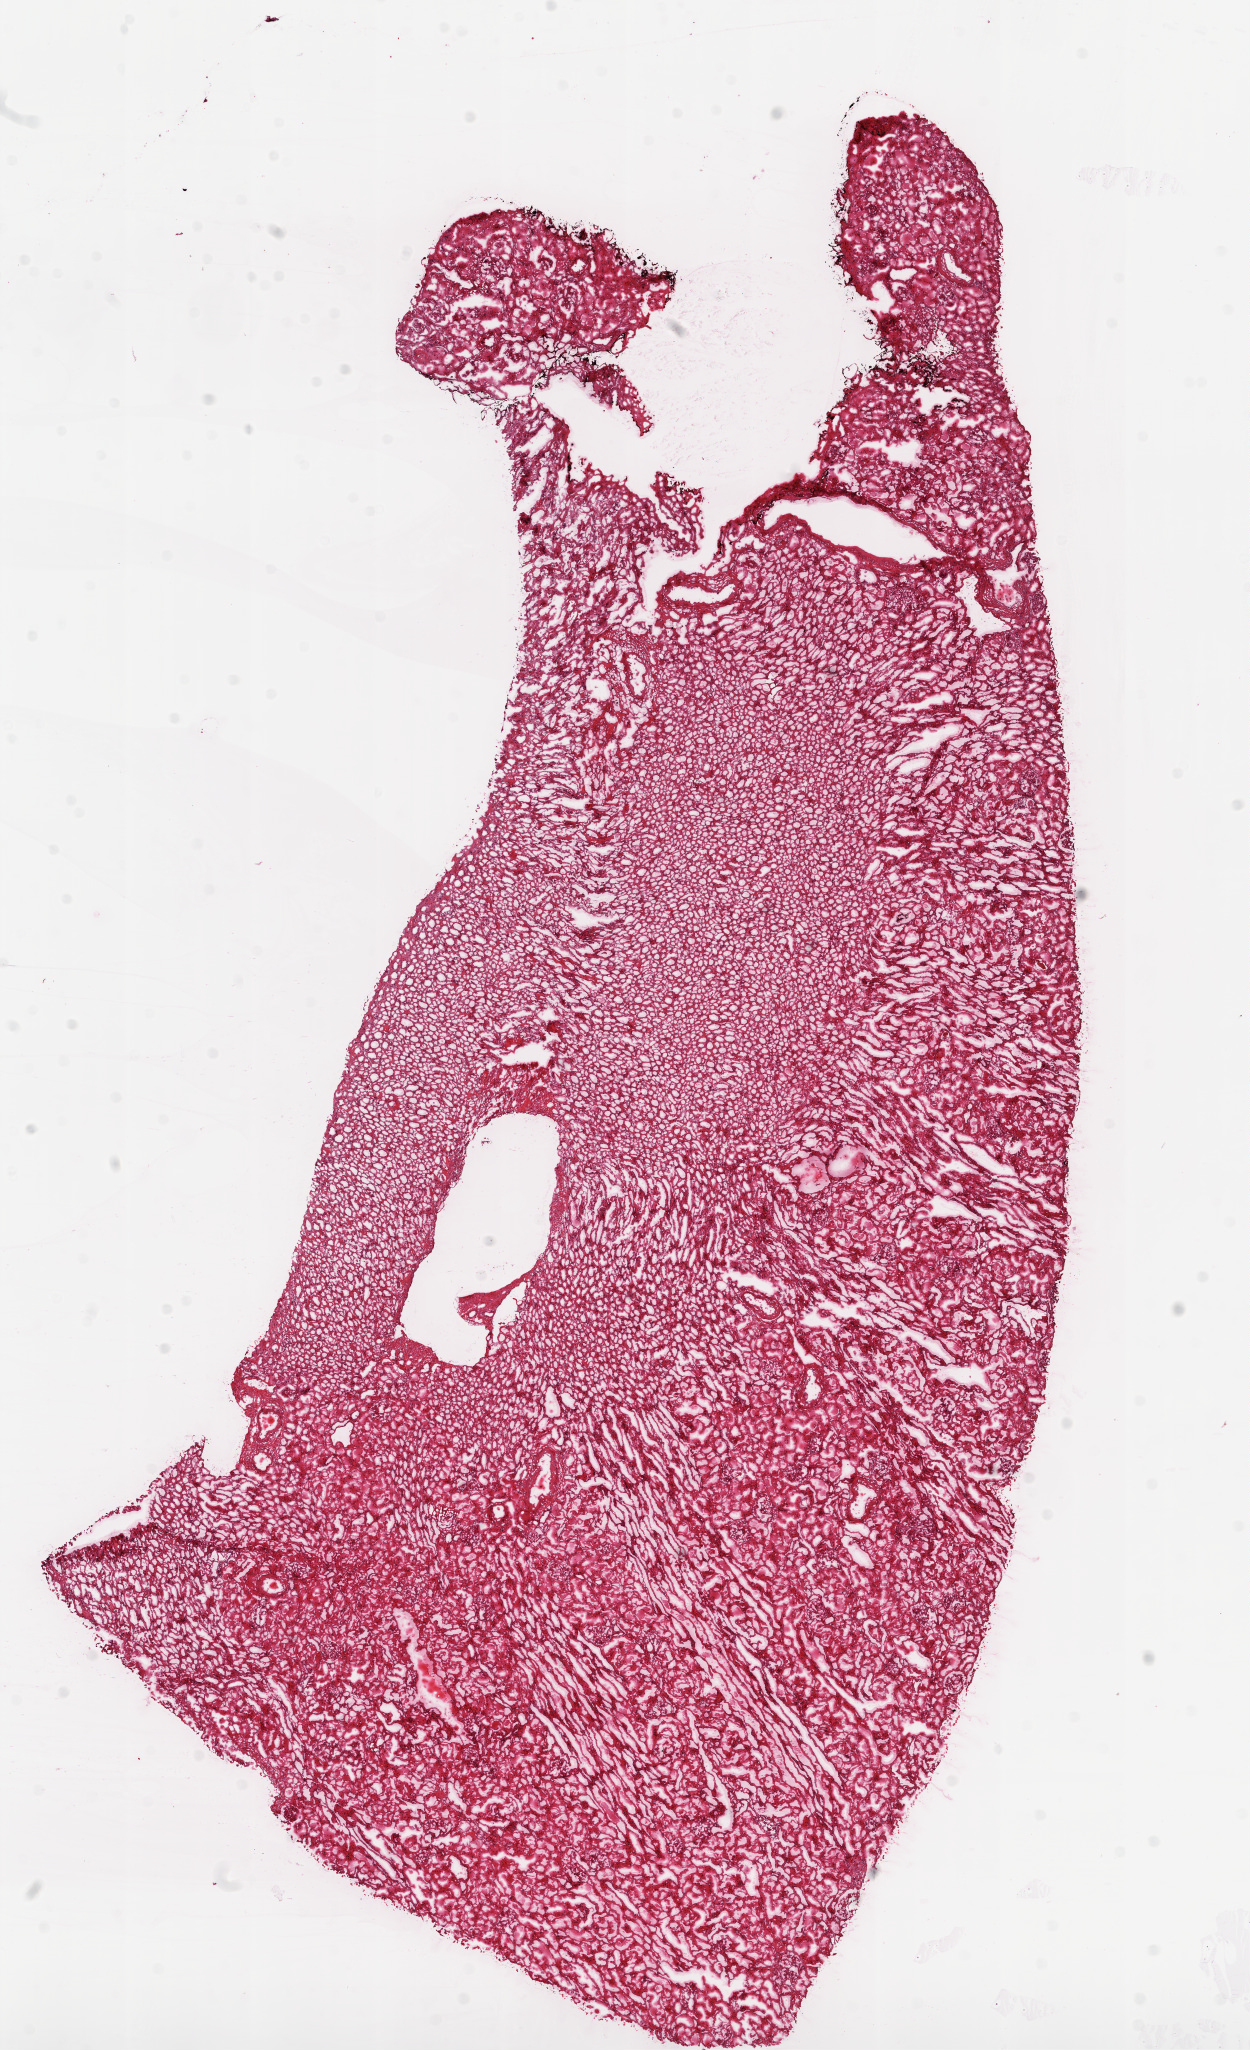
Digitized Hematoxylin and eosin (H&E) stained tissue section (whole slide) — whole scanned area (about 10.0 x 16.4 mm, from a 20x scan) shown as a low-resolution overview; frozen section from the top of the tissue portion; solid tissue normal (non-tumour tissue) sample from the kidney. Male patient; age at initial diagnosis 65 years.
This section: solid tissue normal sample (biorepository sample class). Patient diagnosis: Clear cell adenocarcinoma, NOS.